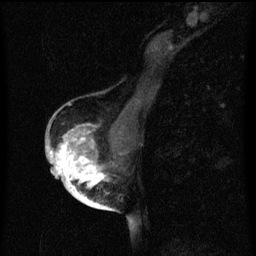
Breast MRI (dynamic contrast-enhanced), one sagittal slice; slice 33 of 60 in the series (ordered by position); dynamic contrast-enhanced series, image 2 of 3 at this slice position (ordered by acquisition); 1.5 T; TE 4.2 ms, TR 8 ms; 2 mm slice thickness; 256 × 256 image matrix, field of view 180 × 180 mm. Patient: female, 56 years.
Outlined on this slice (semi-automatically segmented with operator editing):
- analysis volume of interest (the breast-tissue region the enhancement analysis was run in; not a lesion): box from (x=54, y=126) to (x=120, y=199) px
- tumour enhancement mask (voxels above the 70 % enhancement threshold inside the analysis volume of interest): (x=54, y=126)–(x=108, y=199)